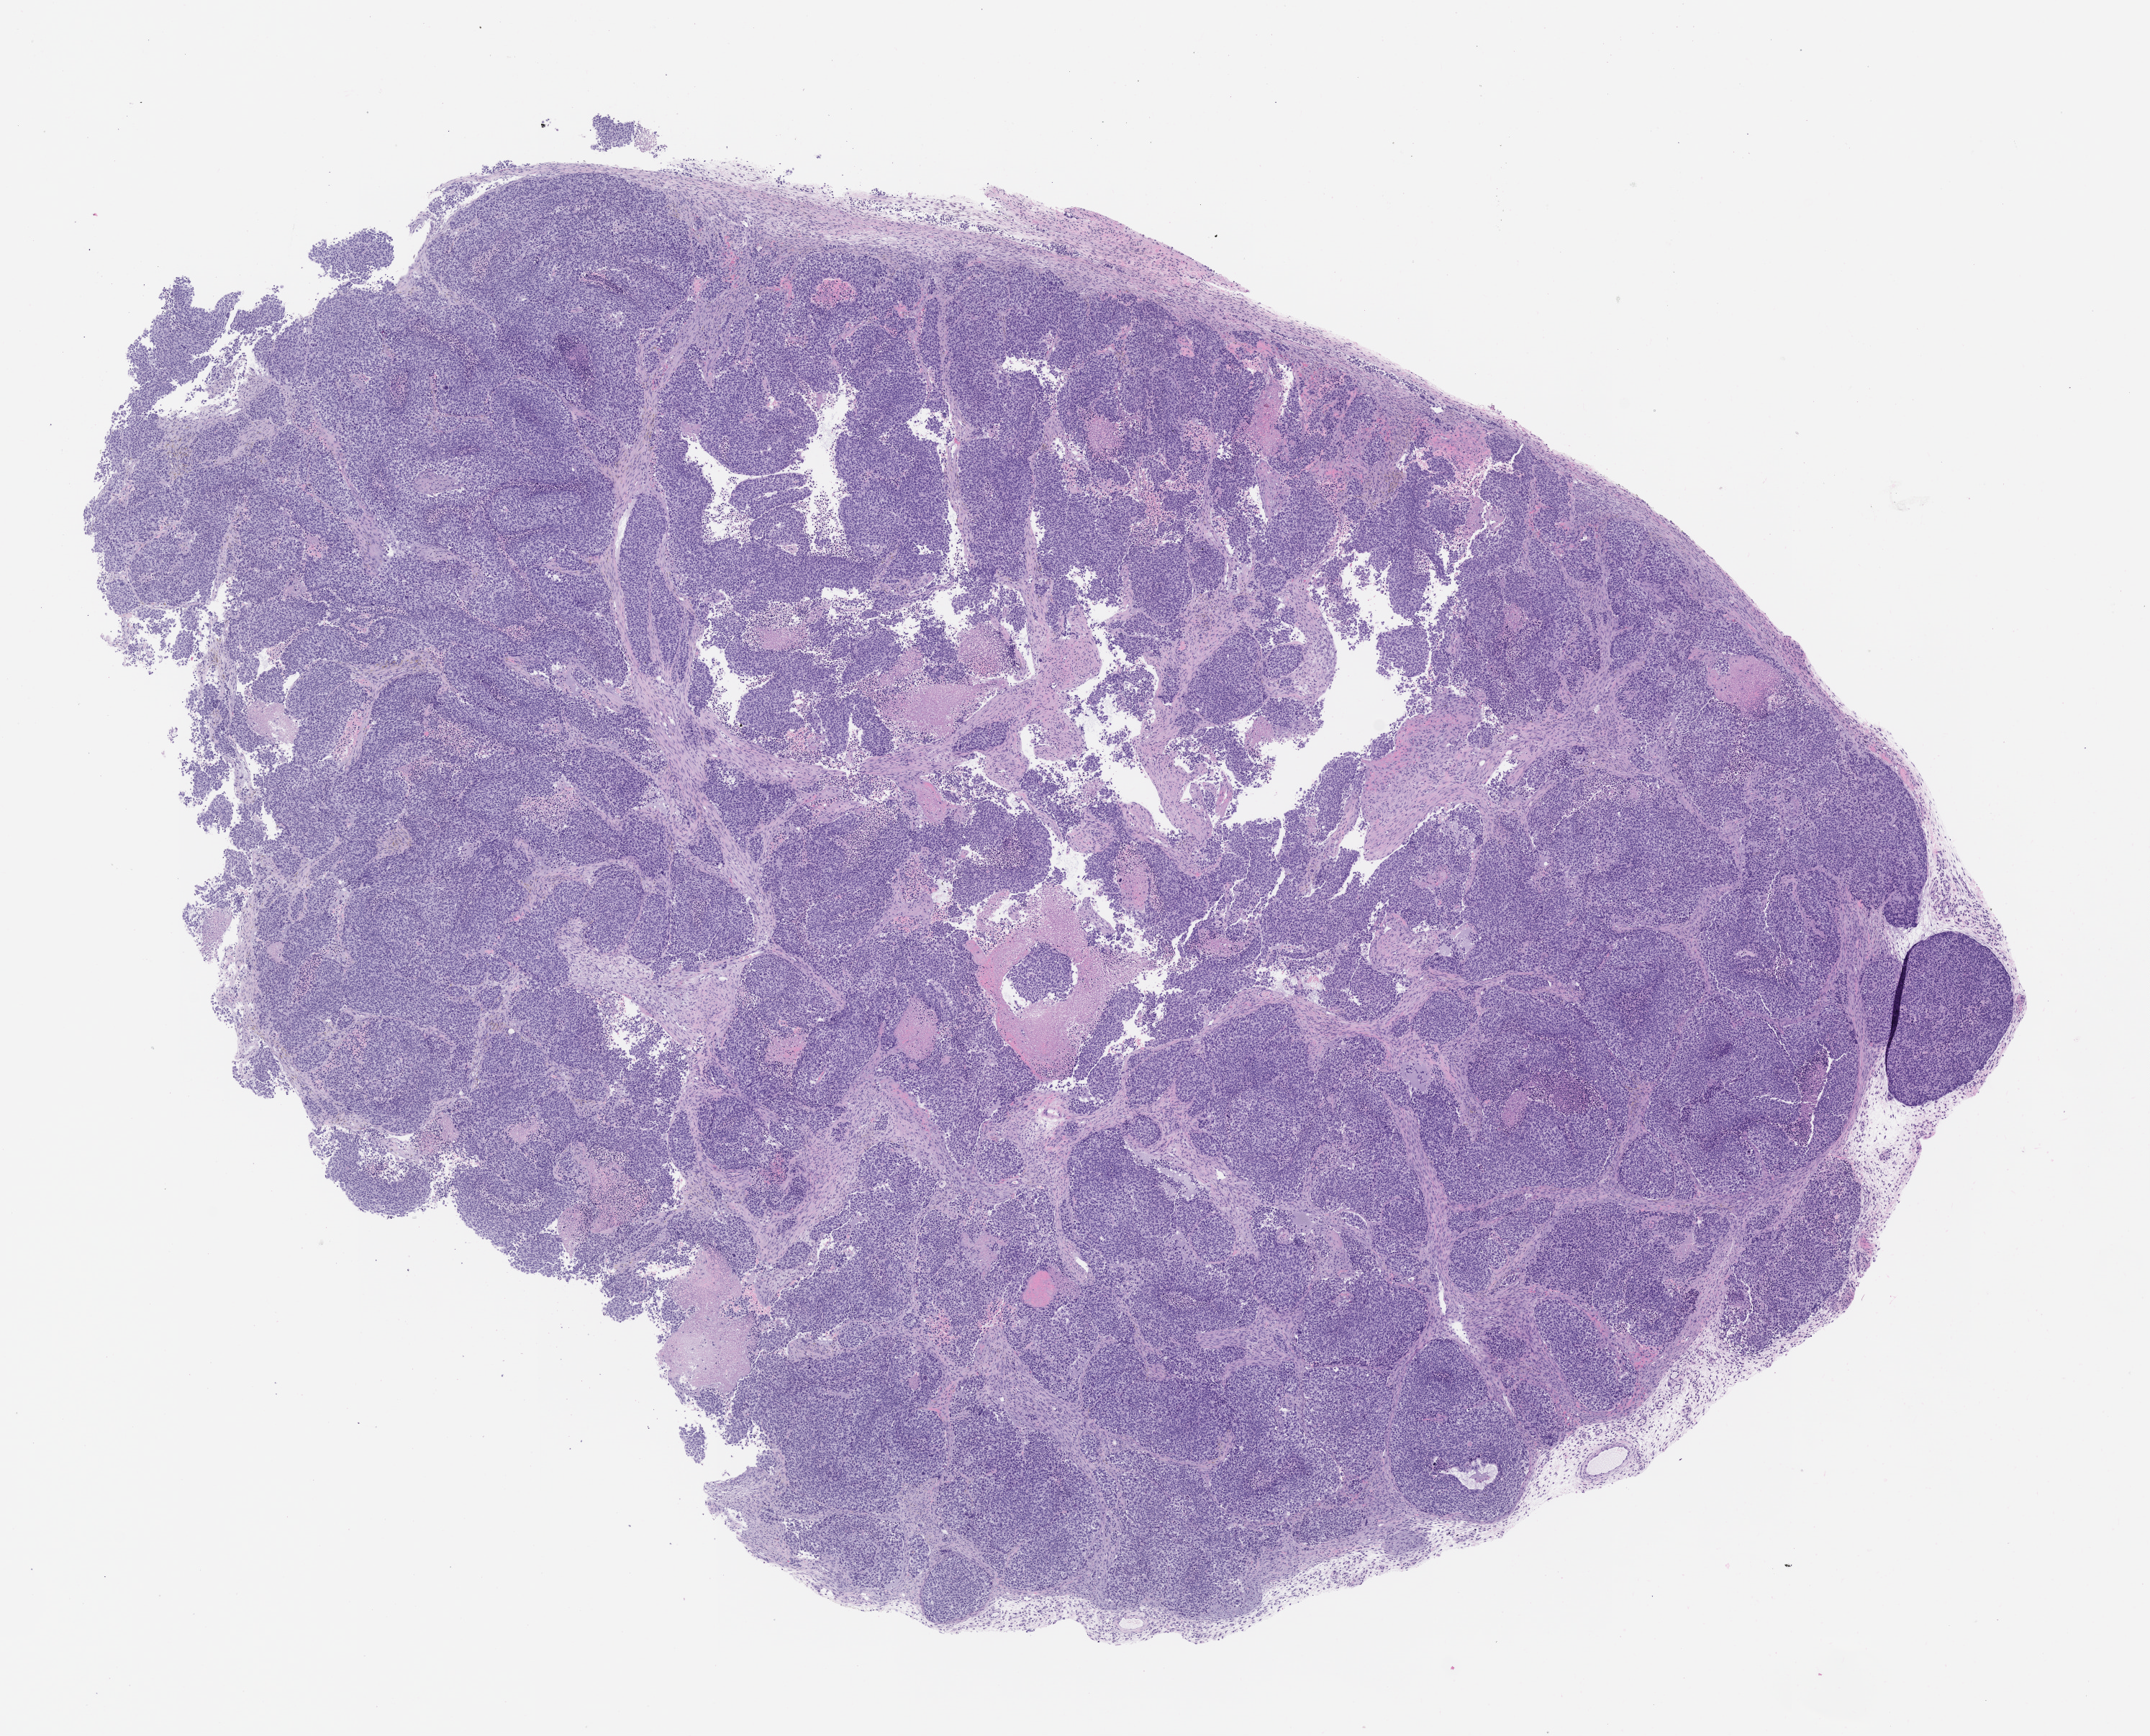
Hematoxylin and eosin (H&E) whole-slide image of a patient-derived xenograft (PDX) tumor grown in a mouse, whole scanned area (about 12.0 x 9.7 mm) shown as a low-resolution overview, formalin-fixed, paraffin-embedded (FFPE) tissue, tumor site category: lung.
• originating patient diagnosis: Lung Adenocarcinoma